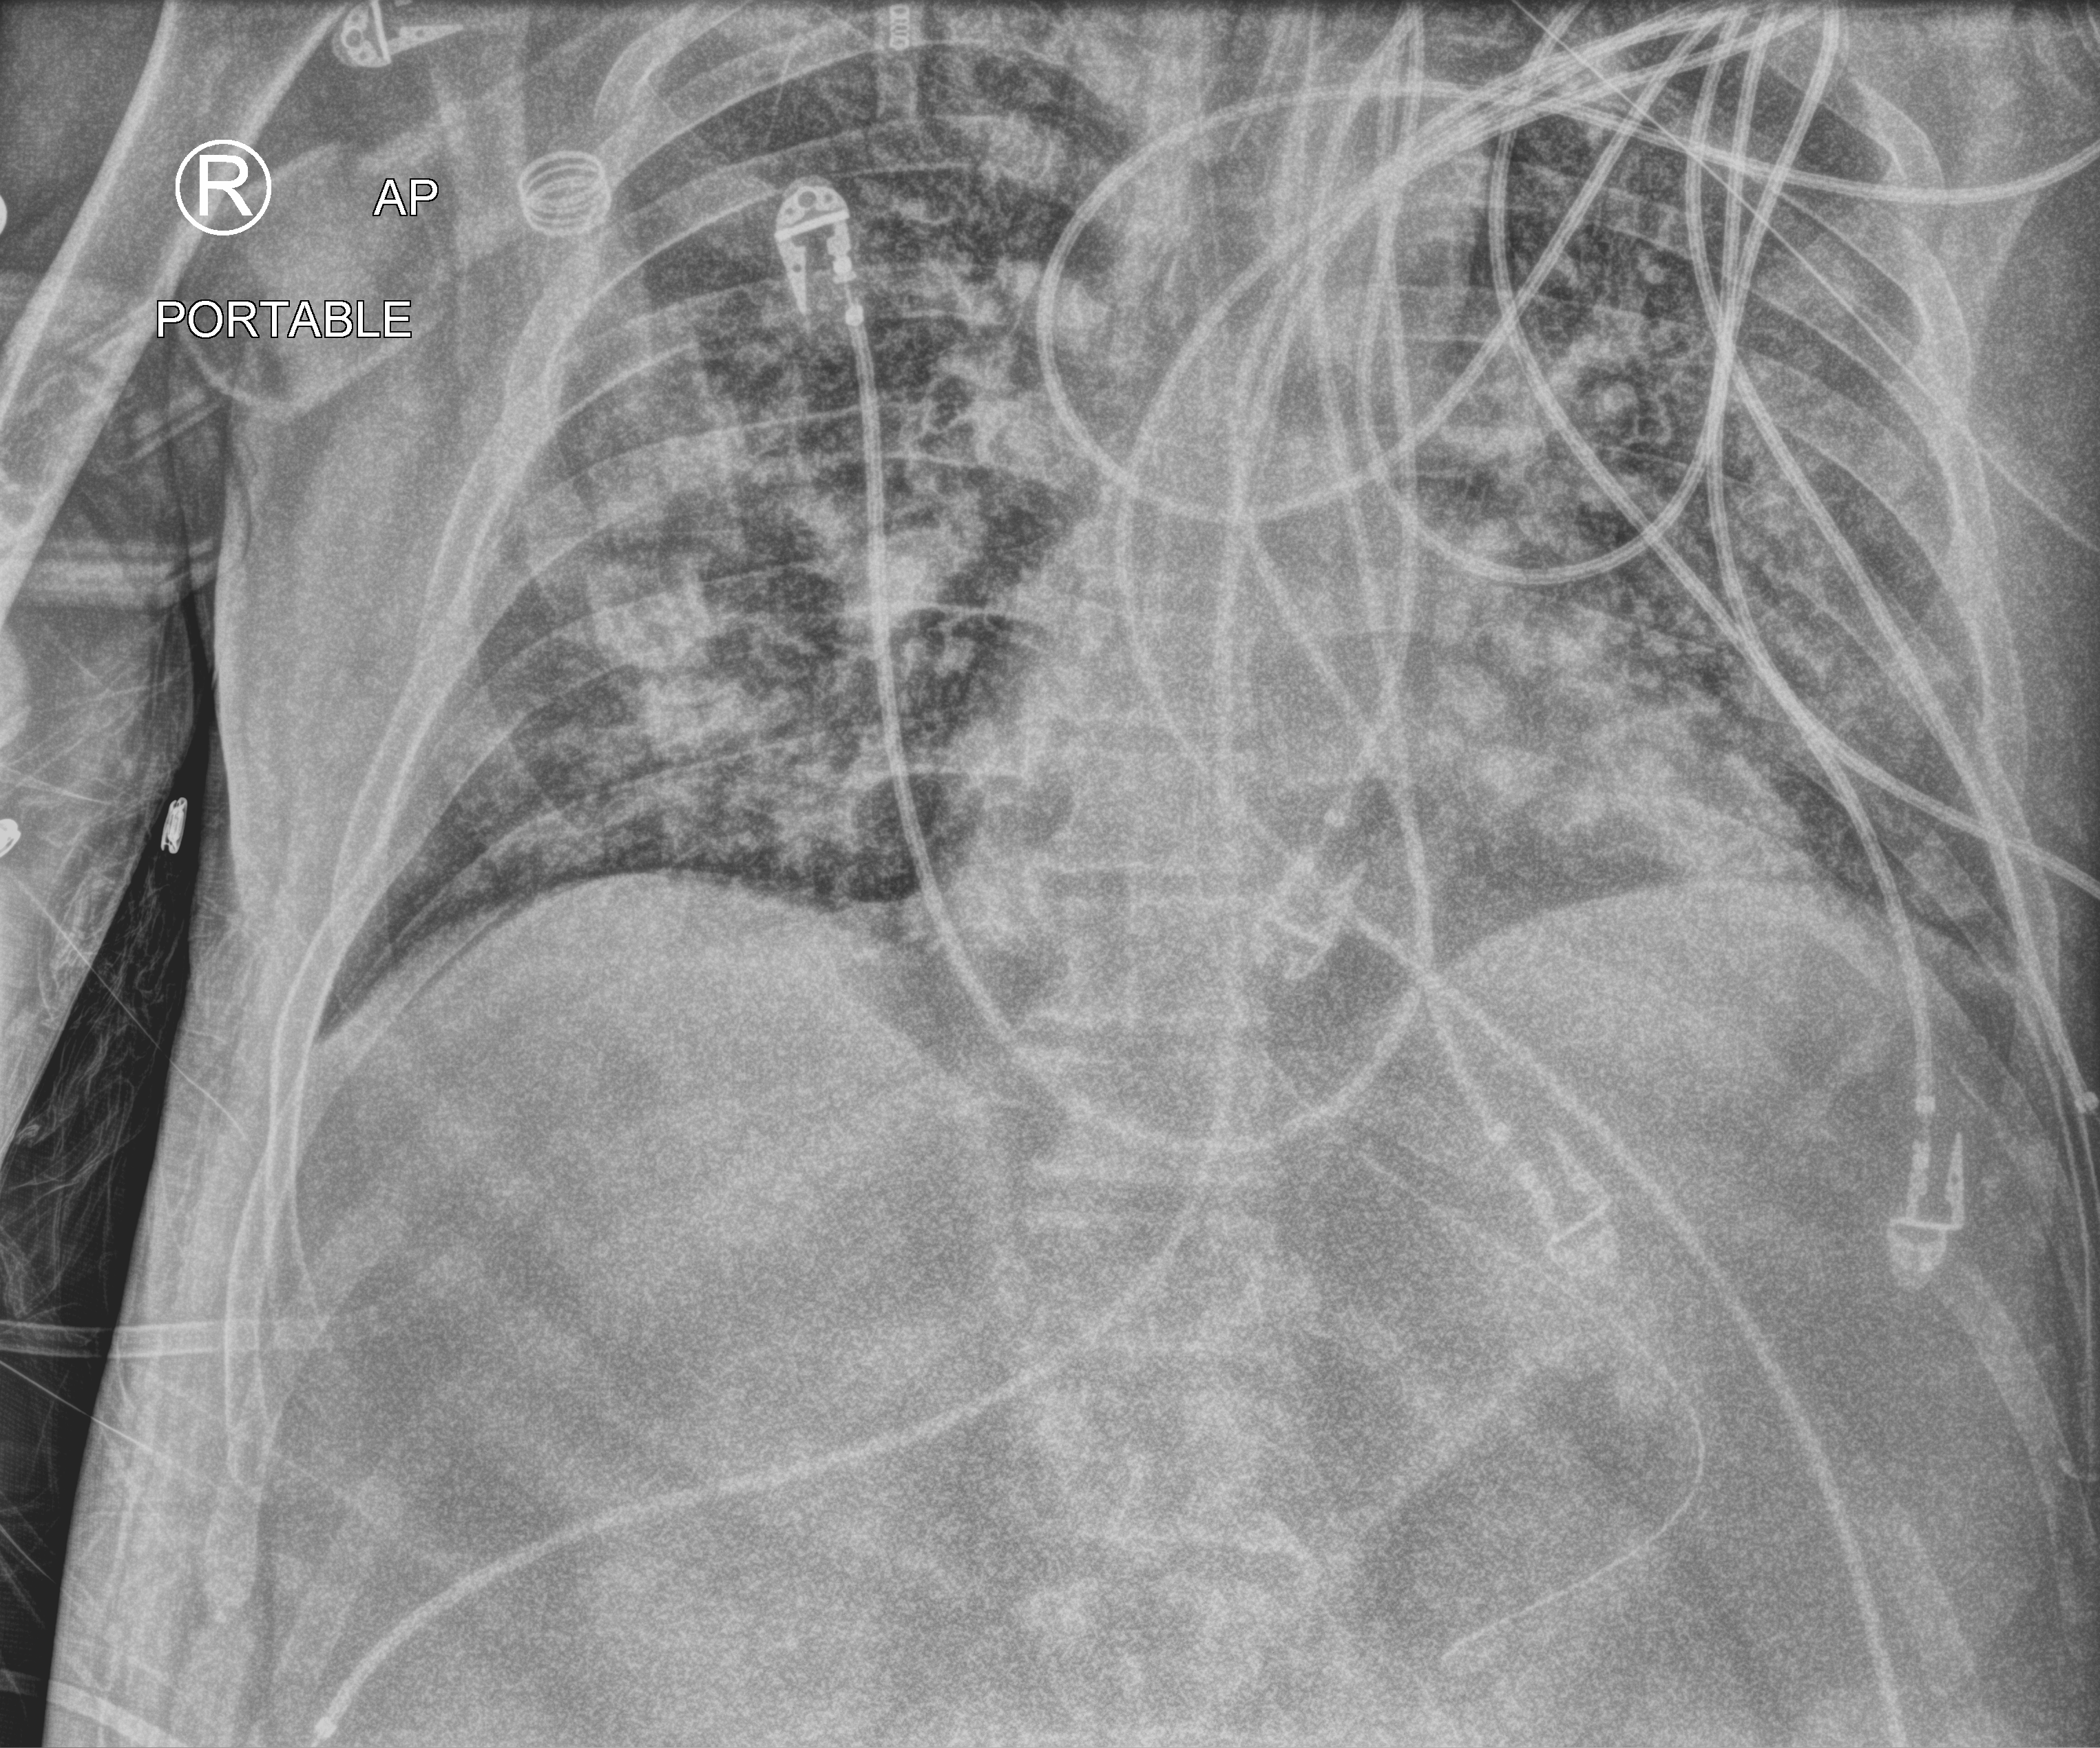
Portable chest radiograph; anteroposterior (AP) projection. Male patient hospitalised with COVID-19, age 18–59 years.
Hospital-stay facts (about this admission, not read from this image; timing relative to this image not recorded): length of hospital stay: 19 days; diabetes (admission record): no.